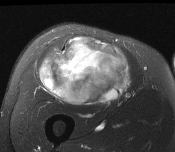
MRI of an extremity soft-tissue mass, one axial slice. Slice 88 of 116 in the series (ordered by position). T2-weighted fat-saturated. MR volume resampled by the dataset authors to the PET/CT grid (not the native acquisition matrix). 175 × 152 image matrix, field of view 171 × 148 mm. Male patient. Case-level facts recorded for this patient, not image findings: histological type: pleiomorphic leiomyosarcoma; grade: intermediate; site of the primary tumour: right thigh.
Outlined on this slice (expert contour drawn on MRI and transferred to this co-registered scan by the dataset authors):
- gross tumour volume including surrounding oedema: box from (x=40, y=38) to (x=130, y=105) px
- gross tumour volume (mass): (x=40, y=38)–(x=130, y=105)